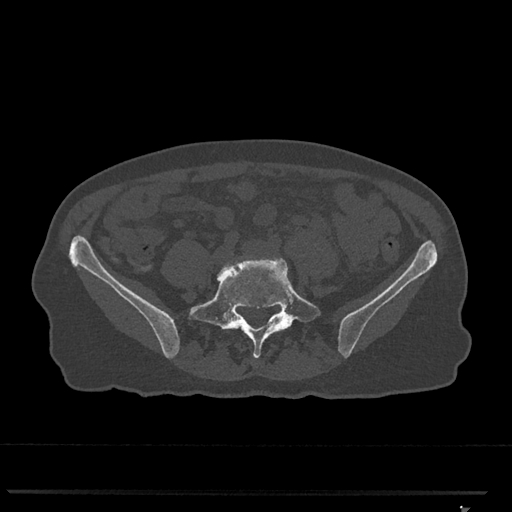
CT including the spine, one axial slice. Slice 157 of 793 in the series (ordered by position). Reconstruction kernel Br40s/3. 120 kVp. Bone window (W 1800 / L 400 HU). 0.5 mm slice thickness. 512 × 512 image matrix, field of view 380 × 380 mm. Female patient, age 62 years. From the clinical record (not read from this slice): primary cancer: renal.
Annotated regions visible in this slice (semi-automatically segmented with operator editing):
- L4 vertebra: bounding box (x1, y1, x2, y2) in pixels: (218, 259, 259, 275)
- L5 vertebra: (189, 258, 321, 358)